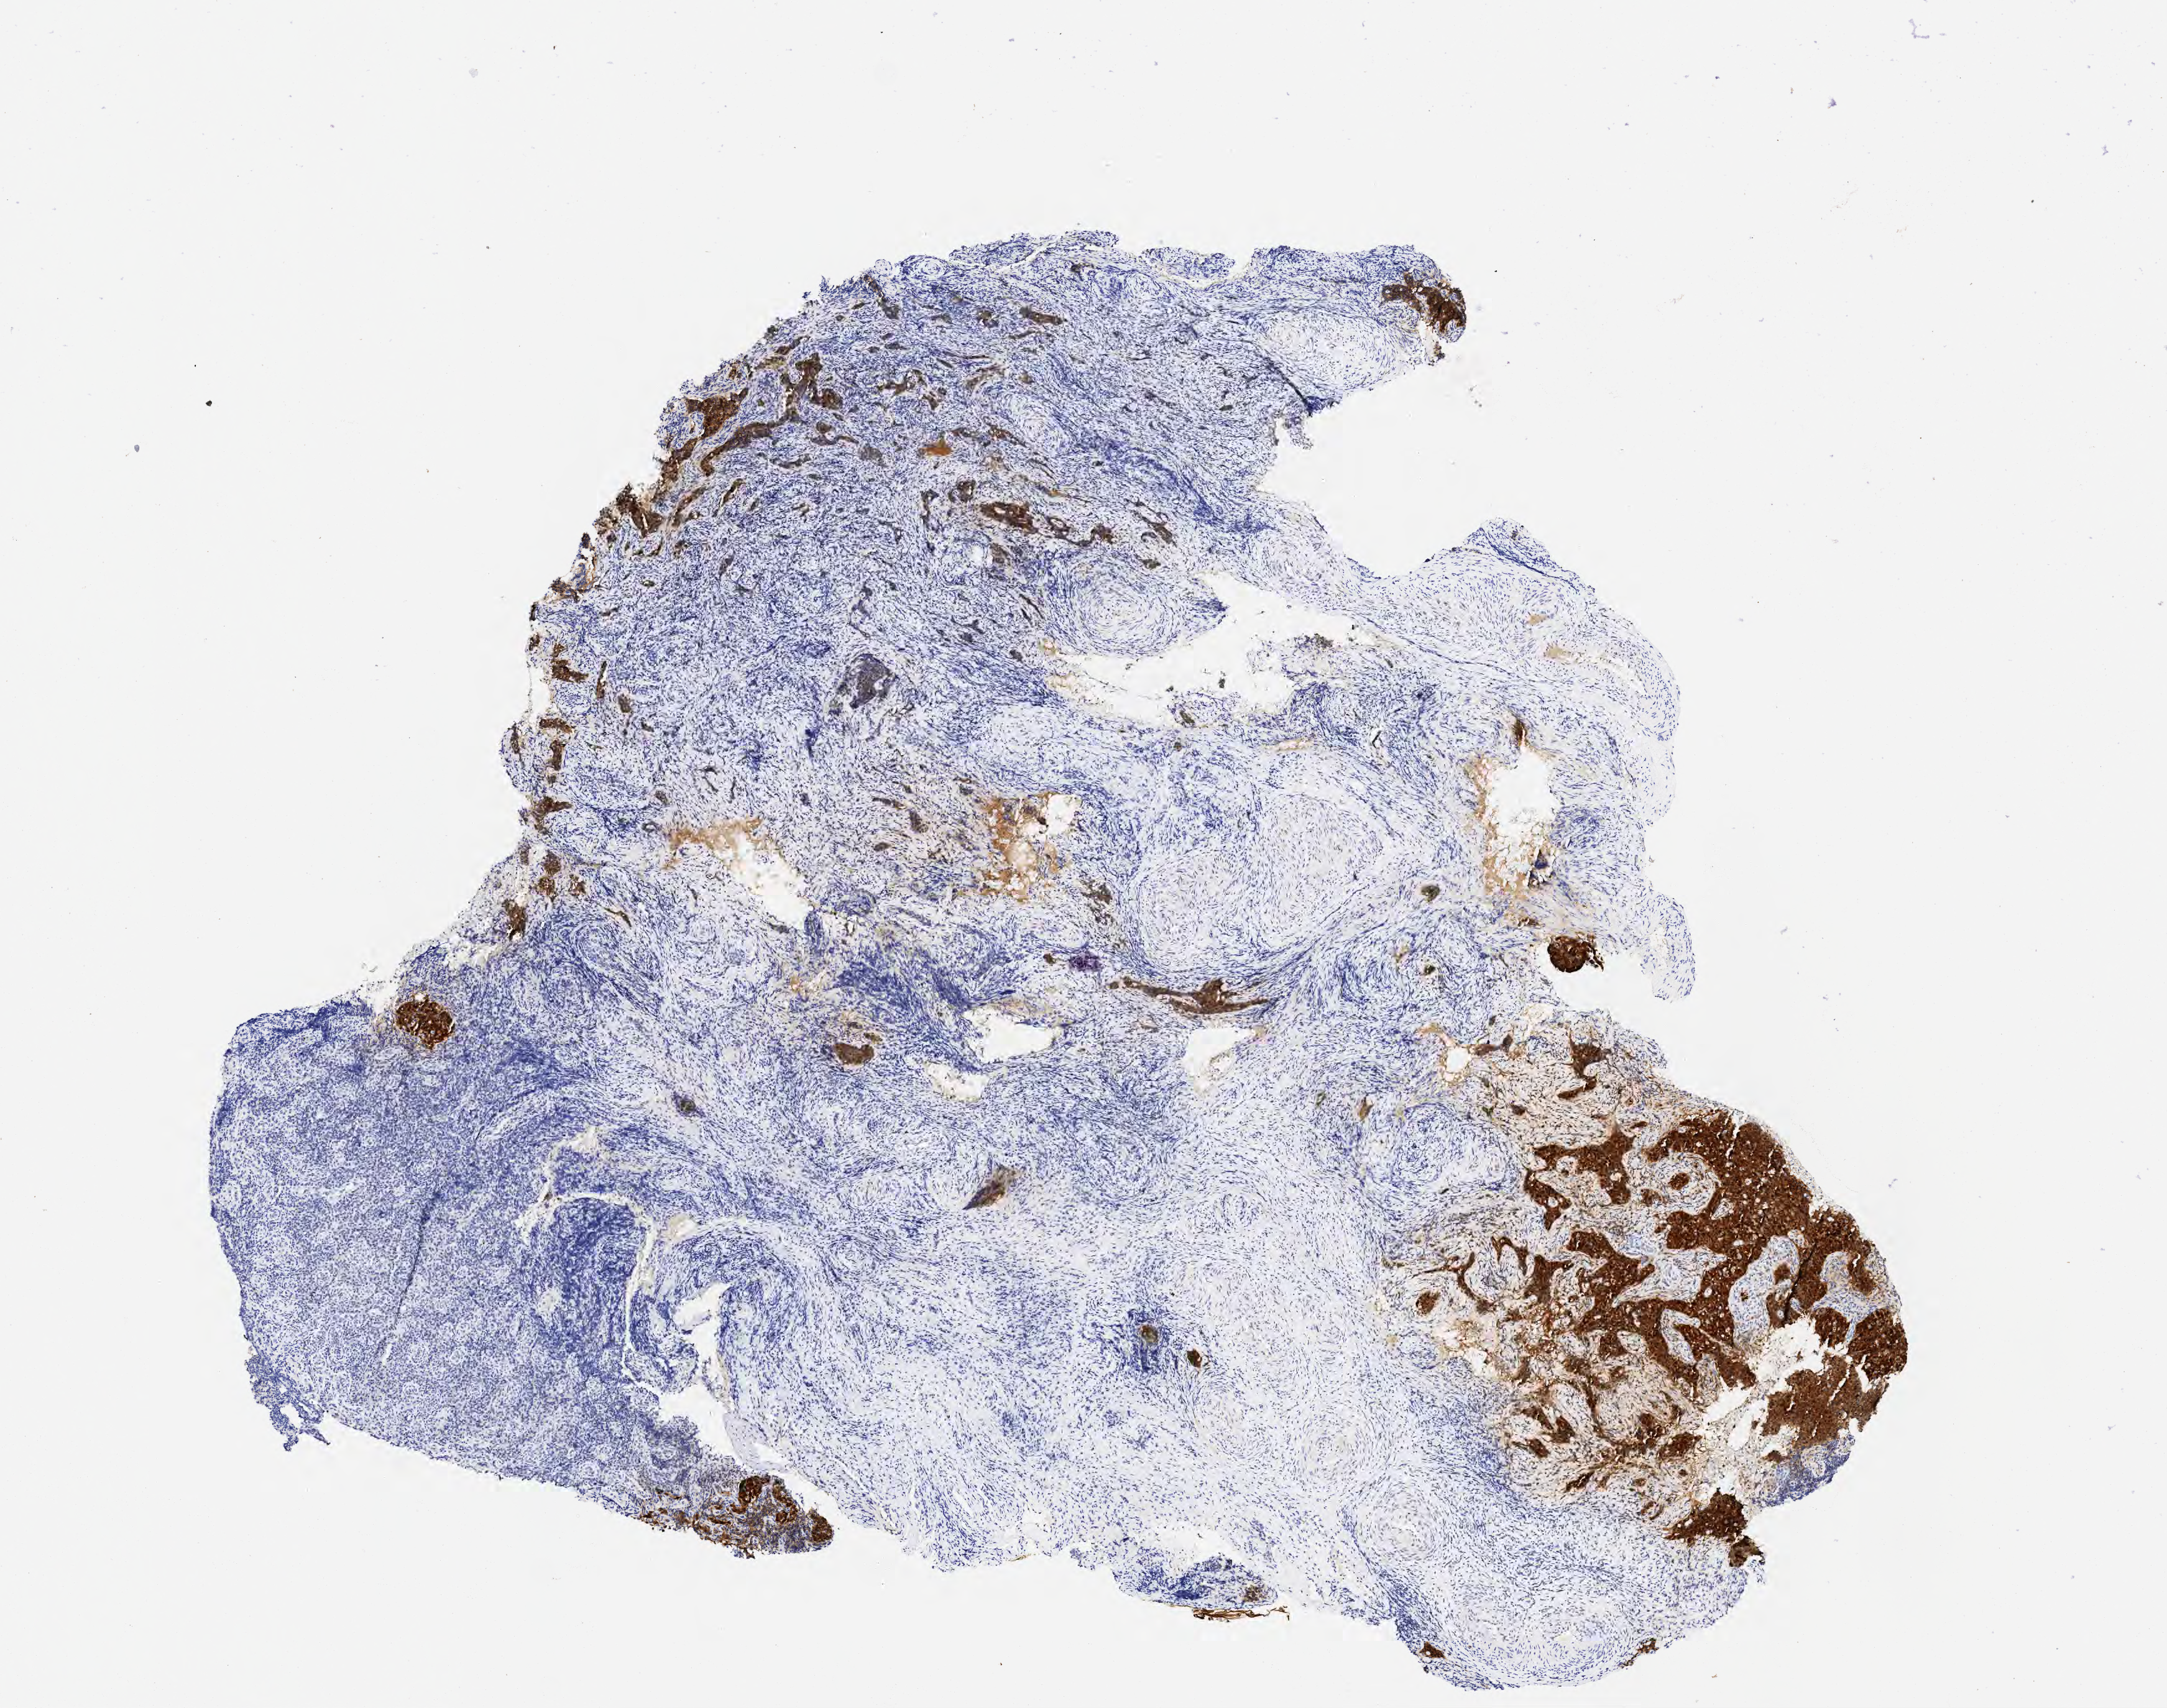
IHC for p16 (p16INK4a), whole-slide image, low-resolution overview of the scanned area, about 7.0 x 5.6 mm; tumor tissue; anatomic site: cervix. Patient female; 31 years old.
Histologic diagnosis: Squamous cell carcinoma, large cell, nonkeratinizing, NOS.